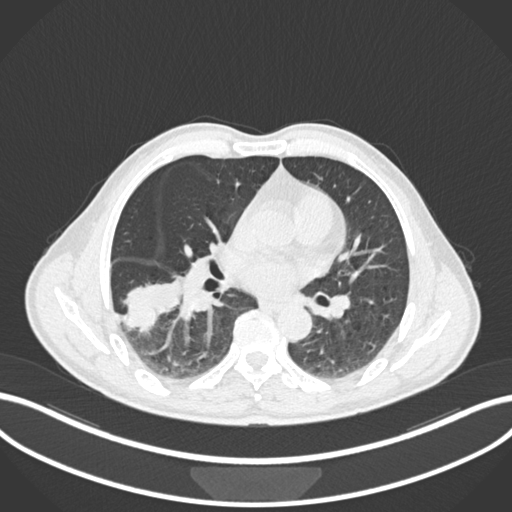
Chest CT, one axial slice. Slice 97 of 208 in the series (ordered by position). Reconstruction kernel B30f. Lung window (W 1500 / L -600 HU). 512 × 512 image matrix. Male patient, age 58 years. Case-level facts recorded for this patient, not image findings: clinical TNM (as recorded): T3 N0 M0; histopathological grade: G2.
Annotated regions visible in this slice (bounding box drawn by a radiologist):
- lung tumour (recorded histology: squamous cell carcinoma): bounding box (x1, y1, x2, y2) in pixels: (117, 269, 185, 333)